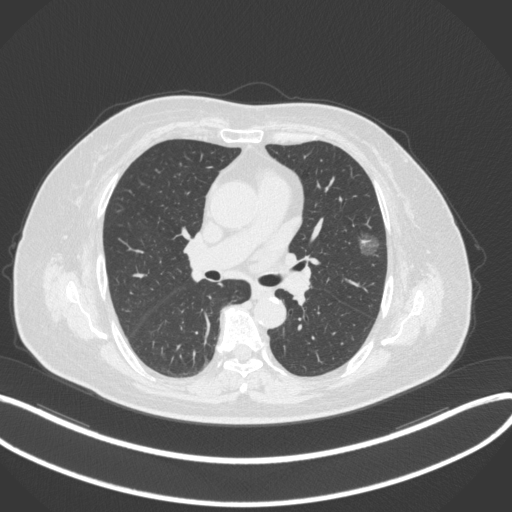
Chest CT, one axial slice. Position 178 of 286 along the scan axis. Reconstruction kernel B31f. Lung window (W 1500 / L -600 HU). 1 mm slice thickness. 512 × 512 image matrix. Patient: female, 76 years. From the clinical record (not read from this slice): clinical TNM (as recorded): T1b N0 M0; histopathological grade: G1-2.
Annotated regions visible in this slice (rectangle marked by the reading radiologist):
- lung tumour (recorded histology: adenocarcinoma): bounding box <353,226,387,258> (left, top, right, bottom; pixels)